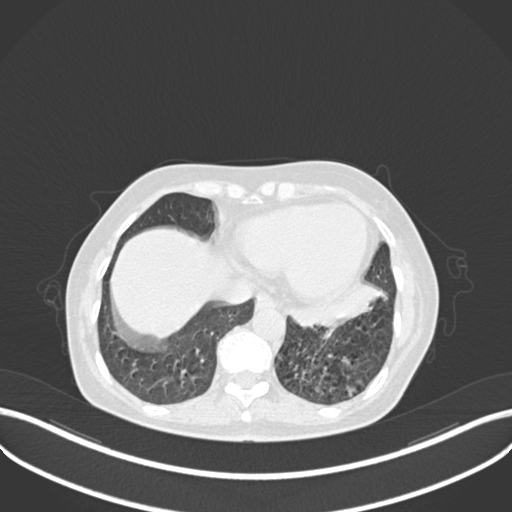
Chest CT, one axial slice. Slice 67 of 270 in the series (ordered by position). 120 kVp. Lung window (W 1500 / L -600 HU). 512 × 512 image matrix, field of view 400 × 400 mm. Patient: female, 63 years. From the clinical record (not read from this slice): clinical TNM (as recorded): T1b N0 M0; histopathological grade: G2-3.
Annotated regions visible in this slice (bounding box drawn by a radiologist):
- lung tumour (recorded histology: adenocarcinoma): bounding box [x1, y1, x2, y2] px = [286, 280, 389, 332]